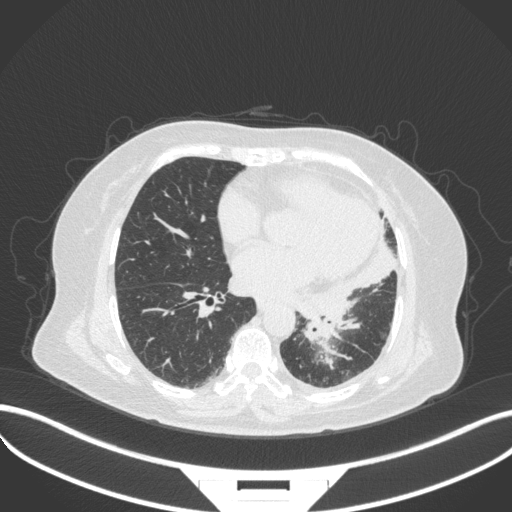
Chest CT, one axial slice; position 149 of 328 along the scan axis; reconstruction kernel B31f; lung window (W 1500 / L -600 HU); 1 mm slice thickness; 512 × 512 image matrix, field of view 400 × 400 mm. Female patient, age 69 years. Case-level facts recorded for this patient, not image findings: clinical TNM (as recorded): T2b N3 M1.
Annotated regions visible in this slice (rectangle marked by the reading radiologist):
- lung tumour (recorded histology: adenocarcinoma): bounding box [x1, y1, x2, y2] px = [300, 313, 355, 345]